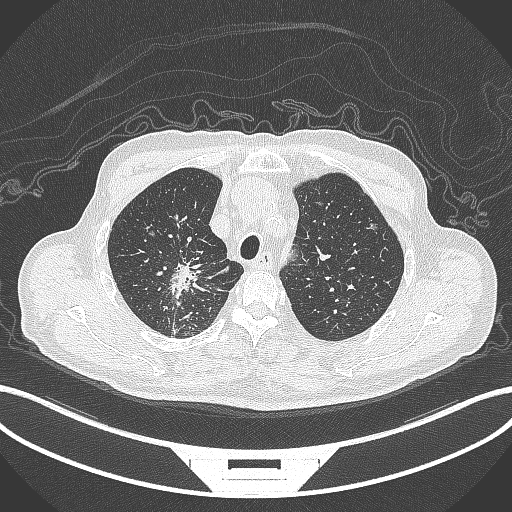
Chest CT, one axial slice; reconstruction kernel B70f; lung window (W 1500 / L -600 HU); 1 mm slice thickness; 512 × 512 image matrix, field of view 400 × 400 mm. Patient: male, 69 years. From the clinical record (not read from this slice): clinical TNM (as recorded): T1c N1 M1.
Annotated regions visible in this slice (rectangle marked by the reading radiologist):
- lung tumour (recorded histology: adenocarcinoma): bounding box (x1, y1, x2, y2) in pixels: (164, 257, 212, 314)